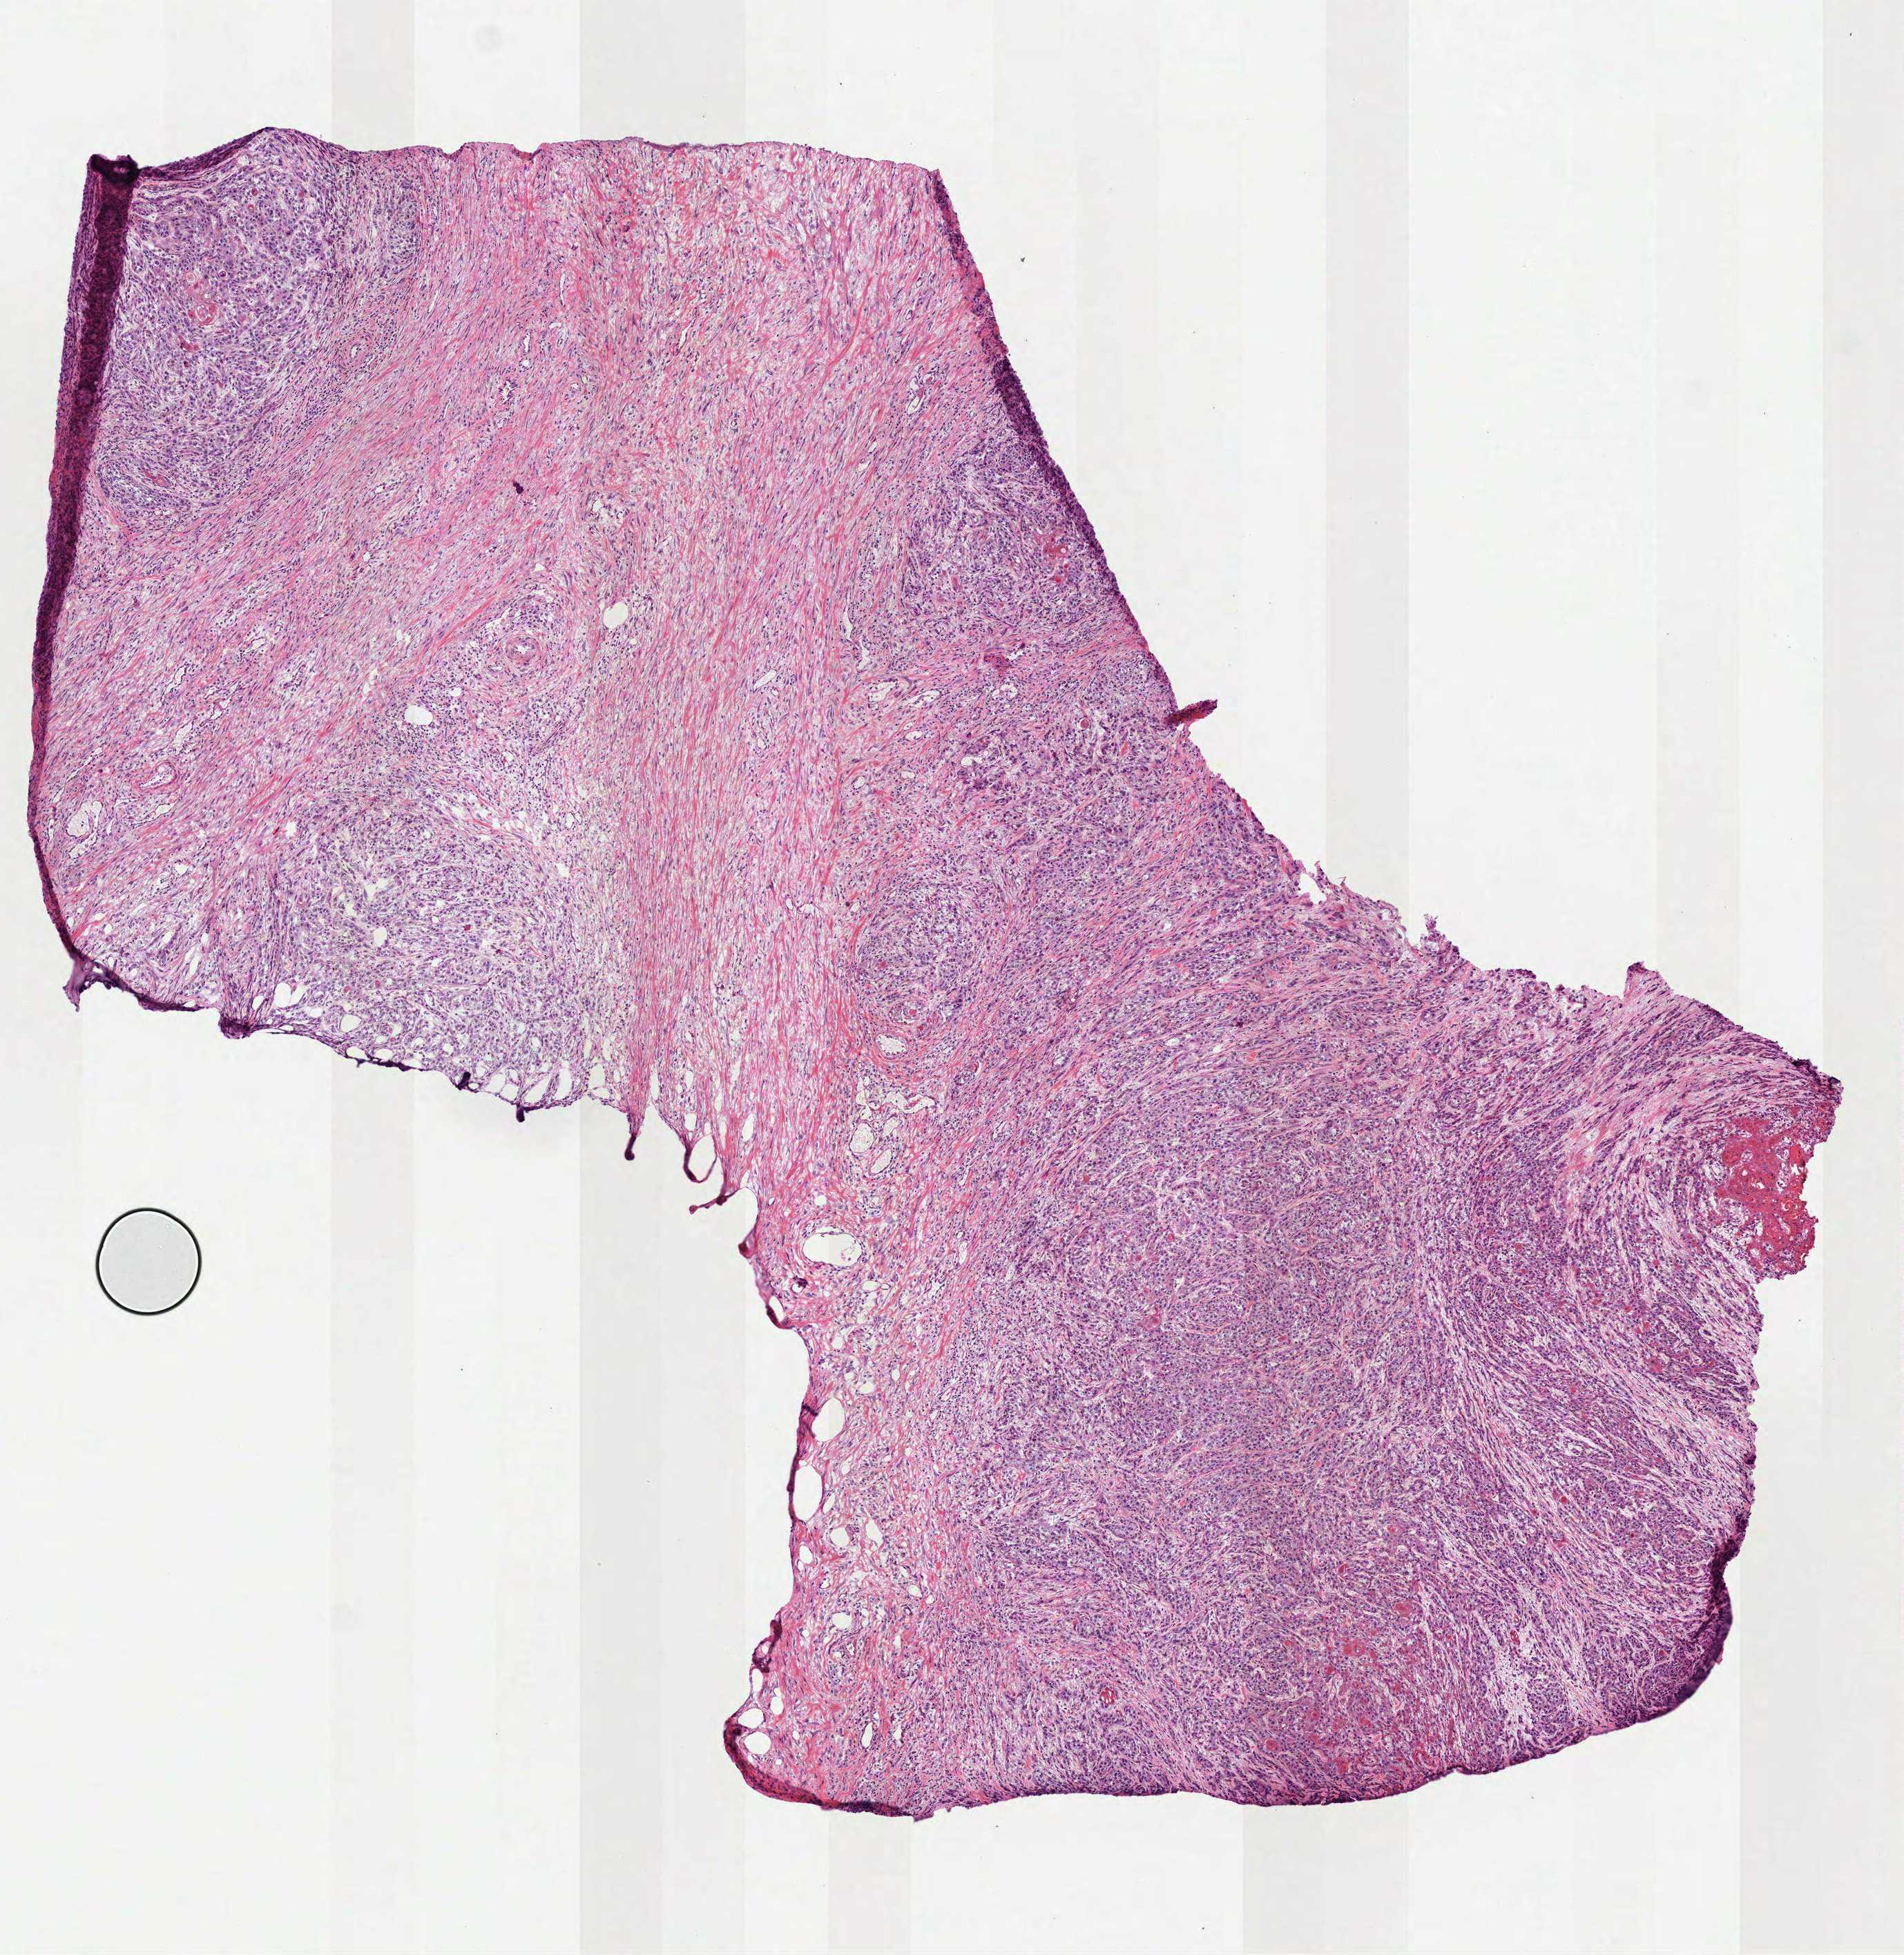
H&E-stained whole-slide image — shown as a low-resolution overview of the whole scanned area (about 5.6 x 5.7 mm); frozen section from the top of the tissue portion; head and neck, primary tumour sample. Male, age 50 years at initial diagnosis. Histologic grade: G2 (moderately differentiated). Pathologist review of this section (percent, as recorded): tumour cells 70%, tumour nuclei 80%, normal cells 0%, stromal cells 30%, necrosis 0%.
AJCC pathologic stage: IVA. Histologic diagnosis: Squamous cell carcinoma, keratinizing, NOS (retromolar area). TNM: T4a N2b M0.